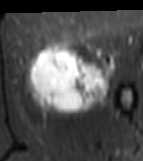
MRI of an extremity soft-tissue mass, one axial slice. STIR. MR volume resampled by the dataset authors to the PET/CT grid (not the native acquisition matrix). 143 × 161 image matrix, field of view 140 × 157 mm. Female patient. From the clinical record (not read from this slice): histological type: myxofibrosarcoma; grade: intermediate; site of the primary tumour: left thigh.
Outlined on this slice (expert contour drawn on MRI and transferred to this co-registered scan by the dataset authors):
- gross tumour volume including surrounding oedema: bounding box <24,40,114,114> (left, top, right, bottom; pixels)
- gross tumour volume (mass): <28,46,112,112>